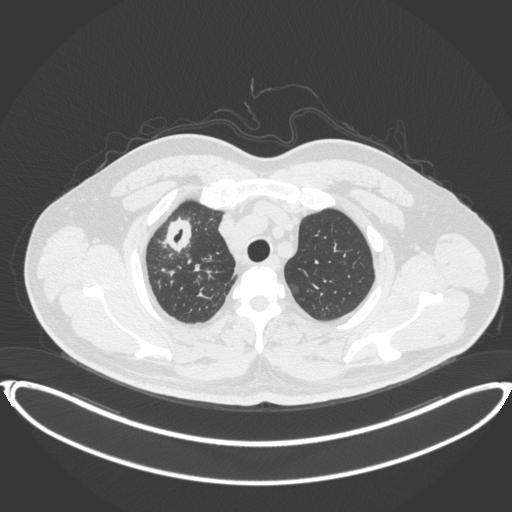
Chest CT, one axial slice; slice 327 of 399 in the series (ordered by position); 120 kVp; lung window (W 1500 / L -600 HU); 512 × 512 image matrix. Male patient, age 53 years. From the clinical record (not read from this slice): clinical TNM (as recorded): T2a N0 M0.
Structures marked on this image (bounding box drawn by a radiologist):
- lung tumour (recorded histology: adenocarcinoma): bounding box (x1, y1, x2, y2) in pixels: (161, 214, 198, 261)